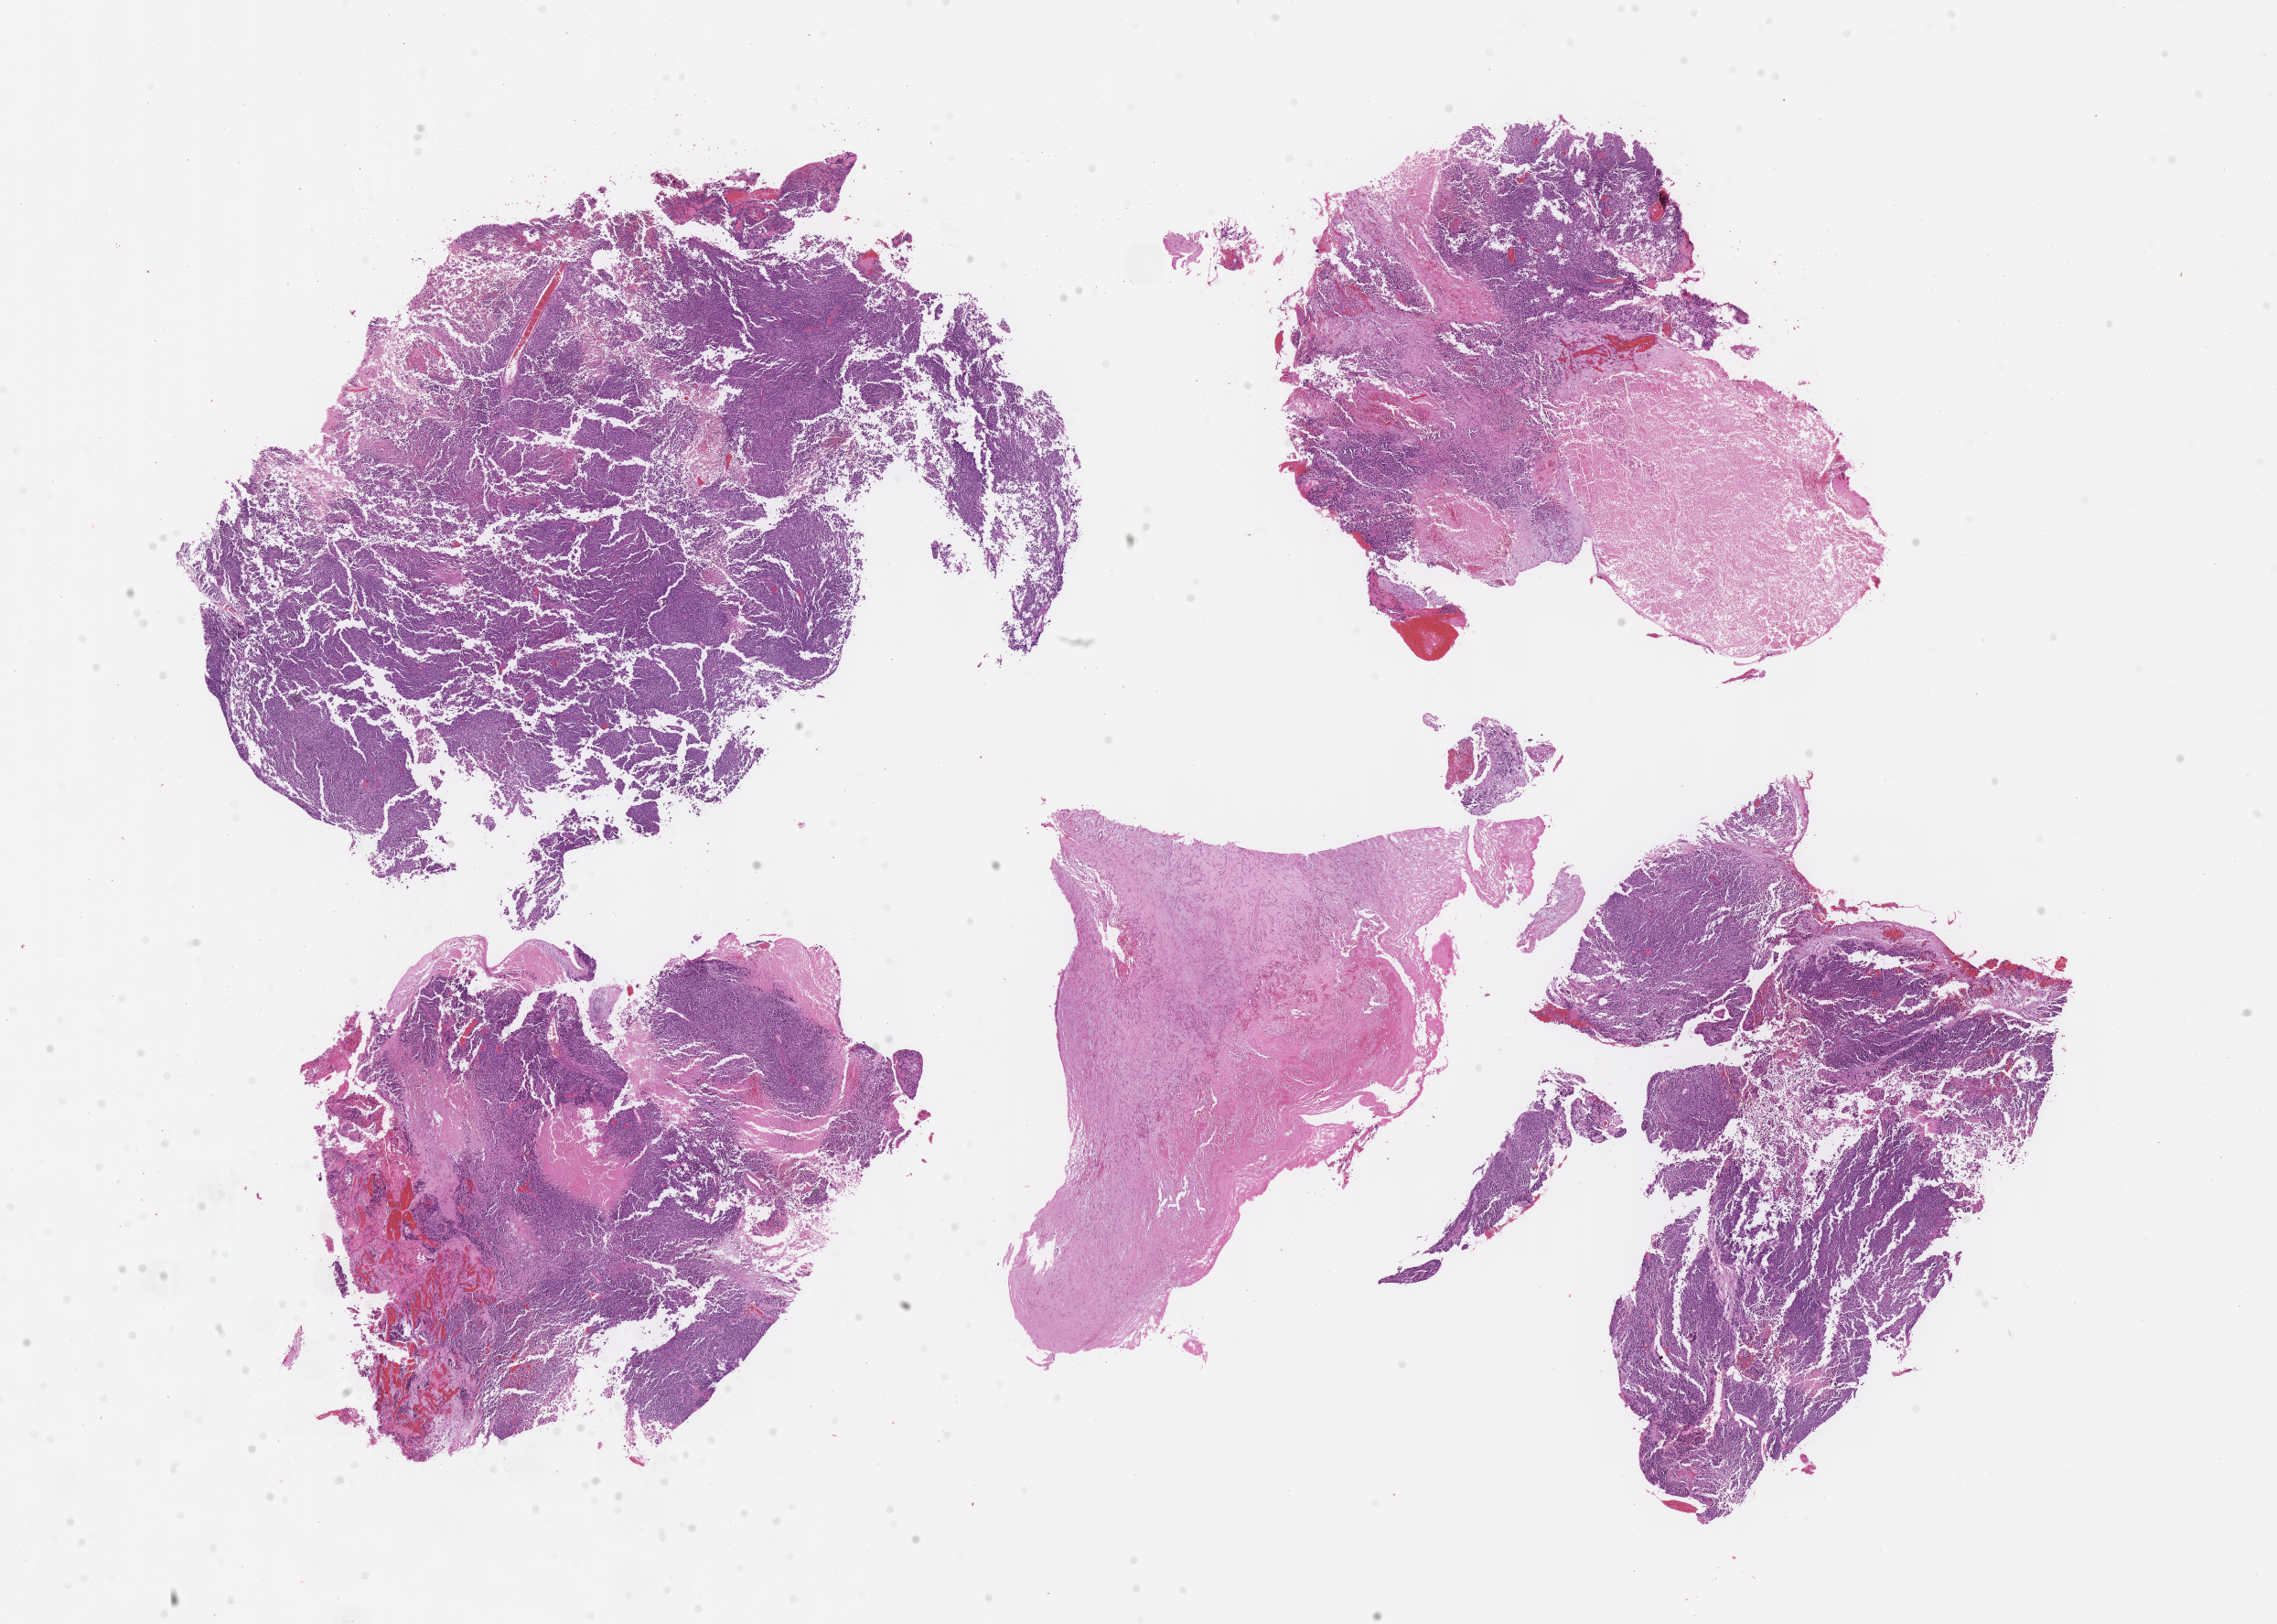
Digitized H&E-stained section of tumor tissue, a low-resolution overview of the entire scanned area, about 20.1 x 14.4 mm. FFPE section. Sample anatomic site: maxillary sinus, right. Patient: female, age 14.4 years at diagnosis.
* metastatic status at presentation (as recorded): non-metastatic
* primary site (case record): paranasal Sinus
* stage (as recorded): 3
* diagnosis: rhabdomyosarcoma; histological classification: alveolar rhabdomyosarcoma